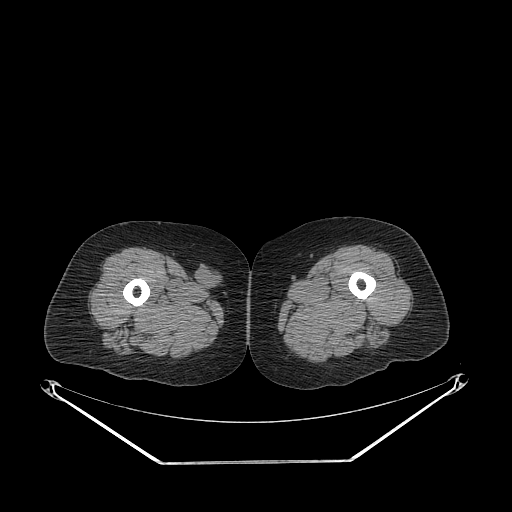
CT of an extremity soft-tissue mass (from a PET/CT study), one axial slice; reconstruction kernel STANDARD; soft-tissue window (W 400 / L 40 HU); 3.75 mm slice thickness; 512 × 512 image matrix, field of view 500 × 500 mm. Female patient. From the clinical record (not read from this slice): histological type: leiomyosarcoma; grade: intermediate; site of the primary tumour: parascapusular.
Annotated regions visible in this slice (expert contour drawn on MRI and transferred to this co-registered scan by the dataset authors):
- gross tumour volume including surrounding oedema: bounding box [x1, y1, x2, y2] px = [194, 263, 222, 289]
- gross tumour volume (mass): [196, 263, 216, 282]